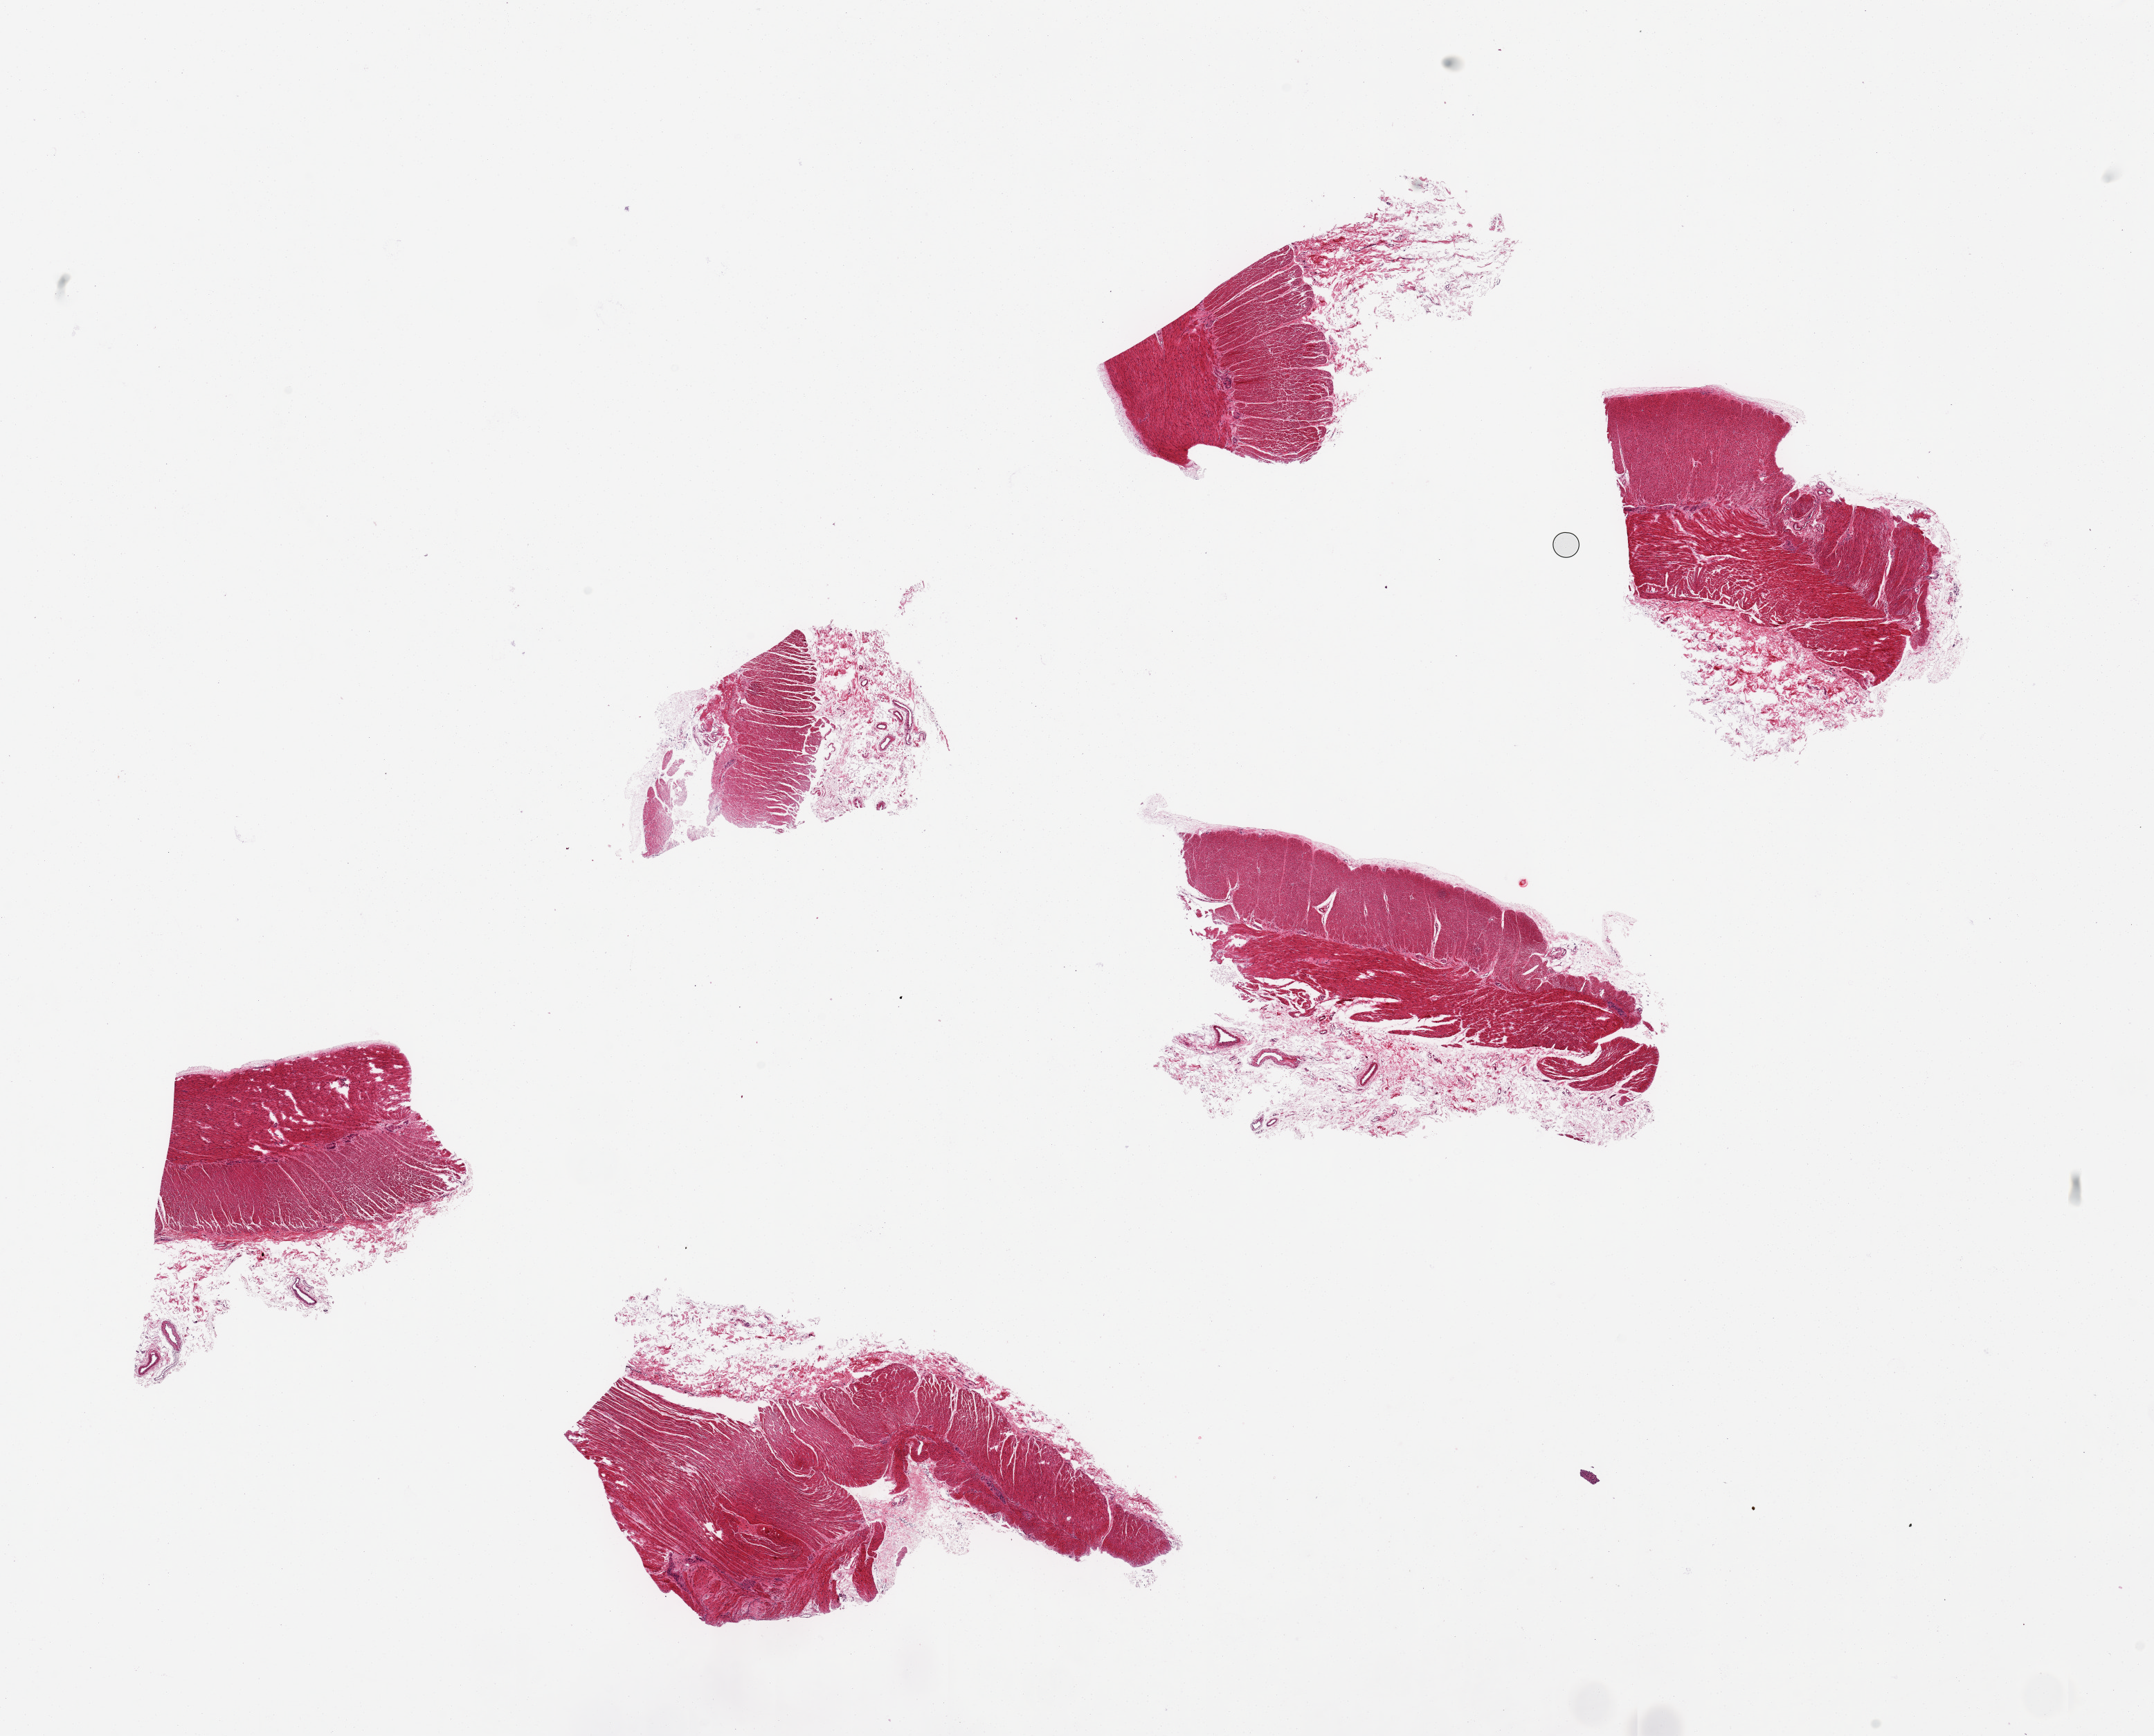
Whole-slide image, haematoxylin and eosin stain, whole scanned area (about 24.6 x 19.8 mm, slide scanned at 20x) shown as a low-resolution overview. PAXgene-fixed paraffin-embedded (PFPE) section. Section of transverse colon (target tissue). Tissue donor sample.
- reviewer comment on this tissue sample: 1. 9 x 3mm pieces (3) No mucosa visible(autolyzed or not); request block rotation; r/o embedding issue